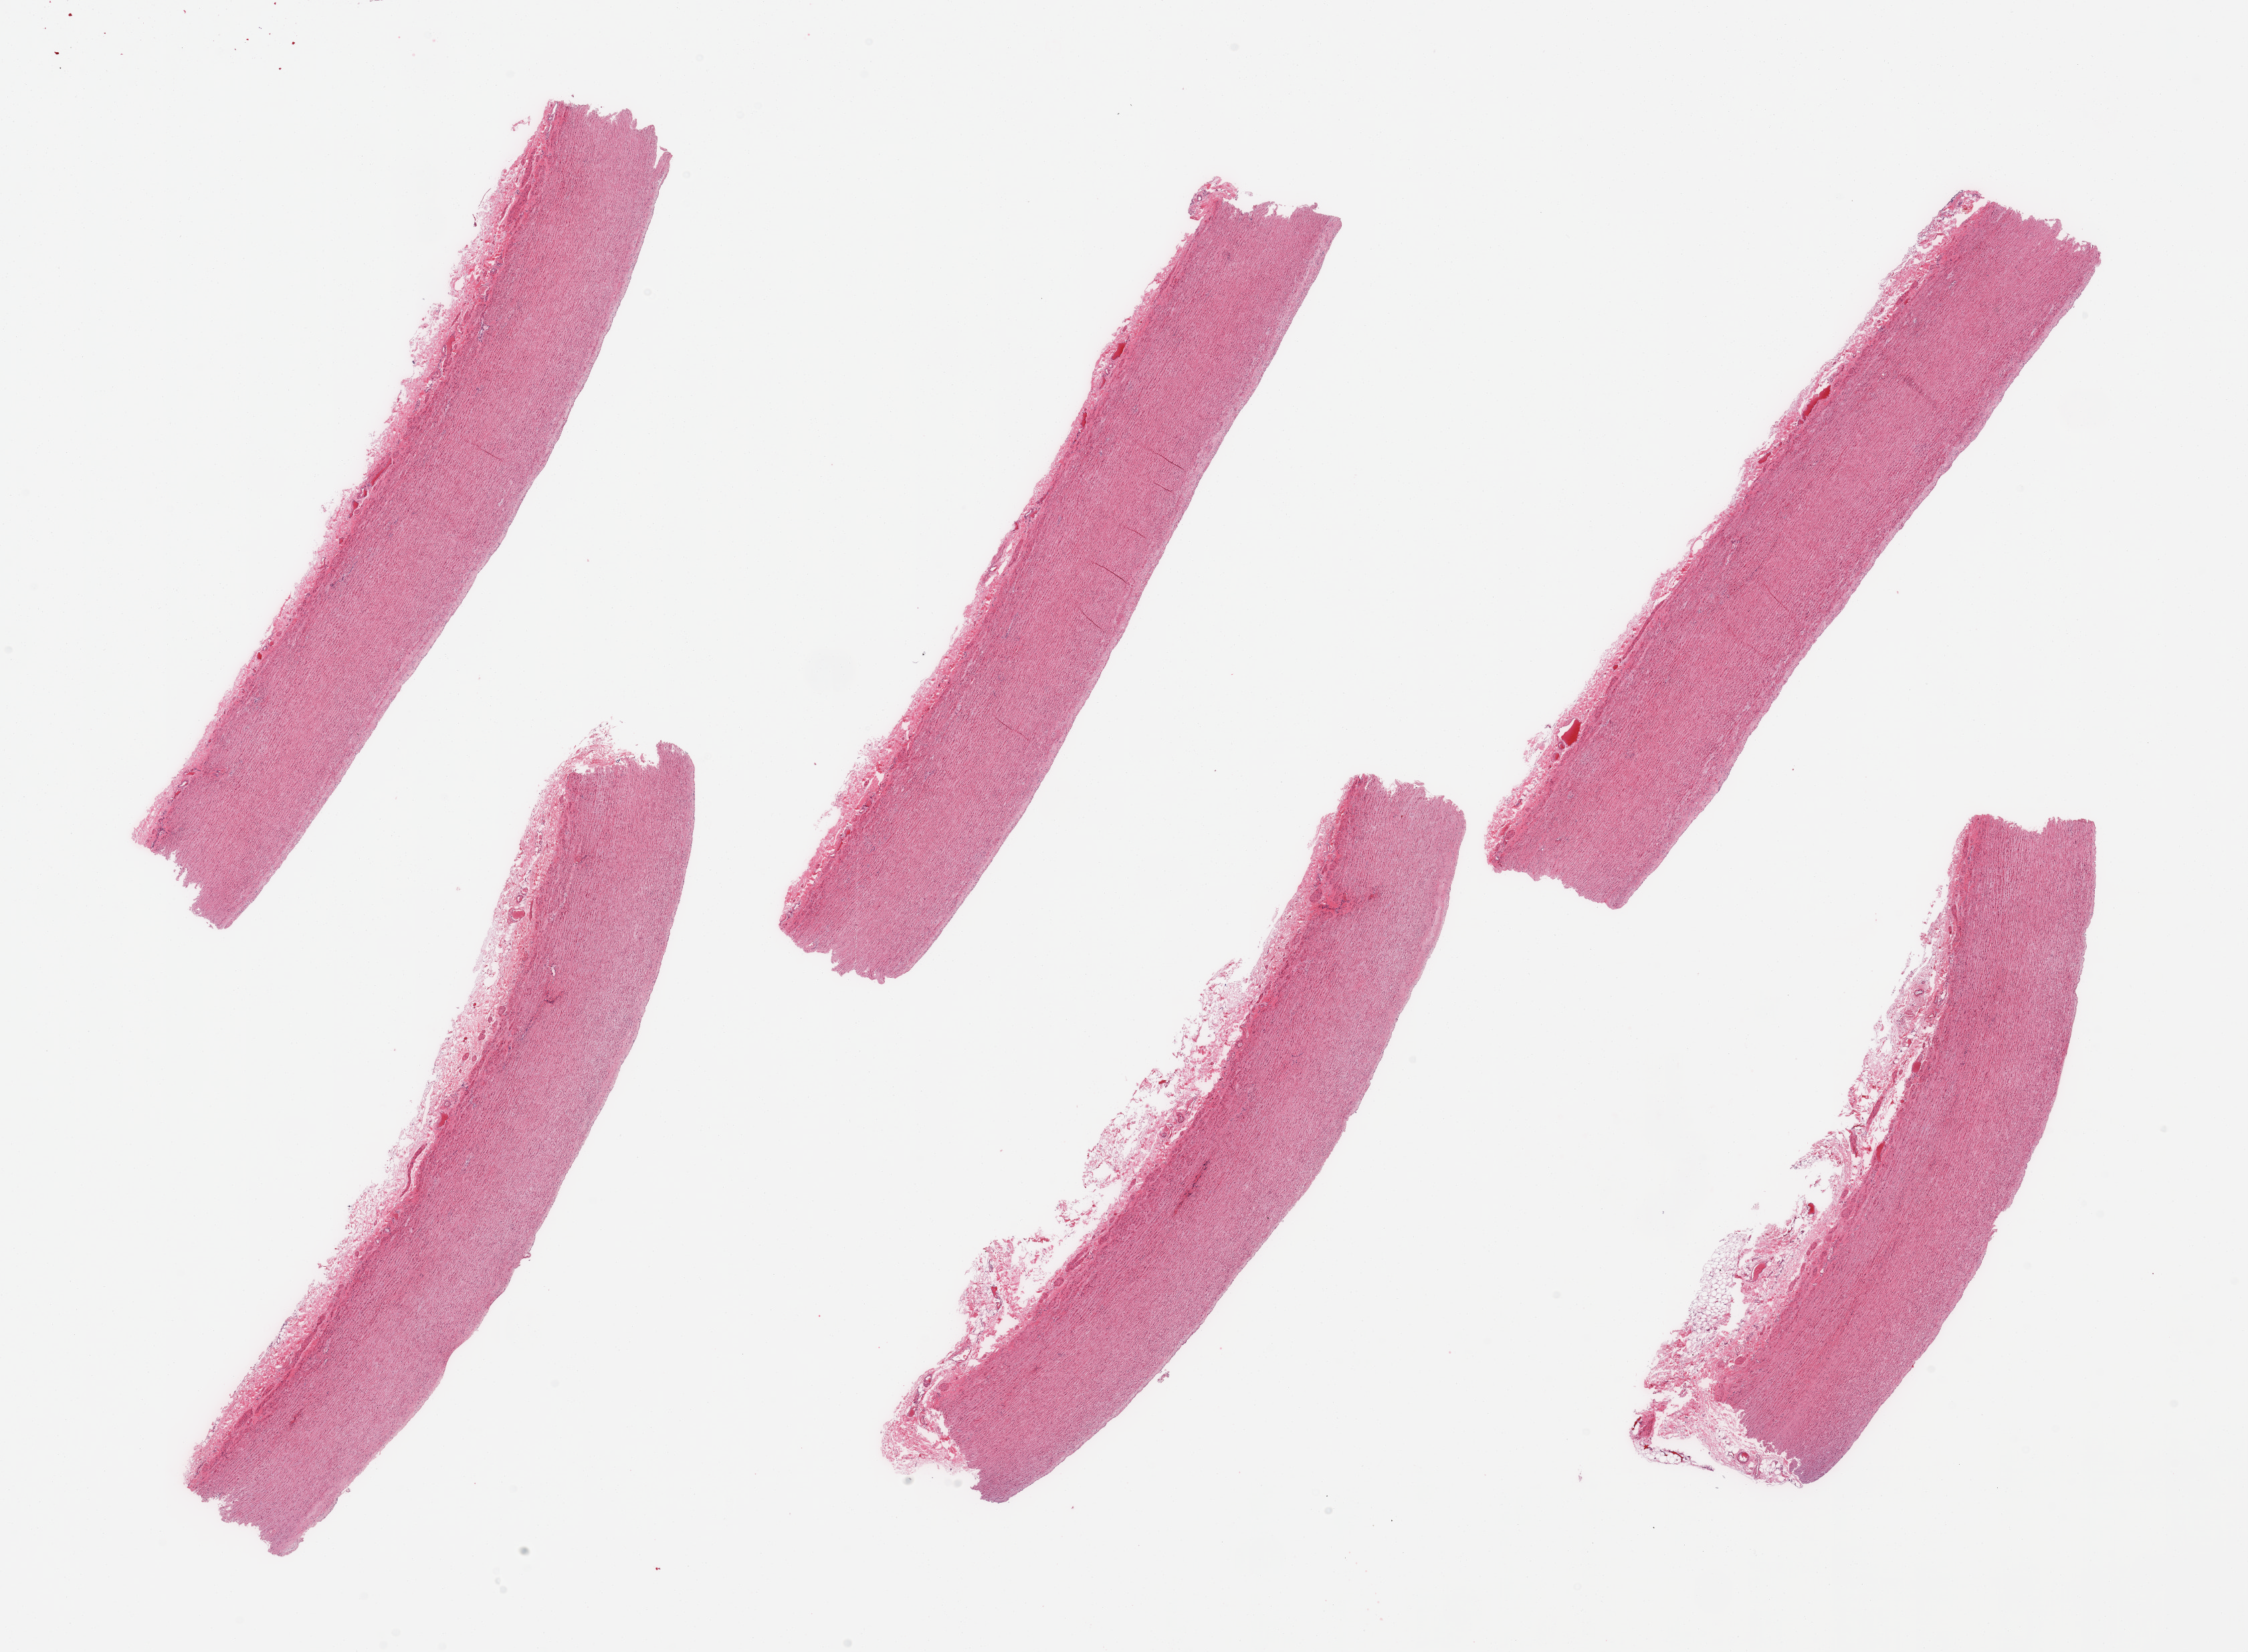
Whole-slide image, H&E stain — whole scanned area (about 26.6 x 19.5 mm, acquisition: 20x scan) shown as a low-resolution overview; PAXgene-fixed paraffin-embedded (PFPE) section; section of aorta (target tissue); tissue donor sample. Donor: male.
Pathologist's review note for this sample: 6 pieces; minimal atherosclerosis.